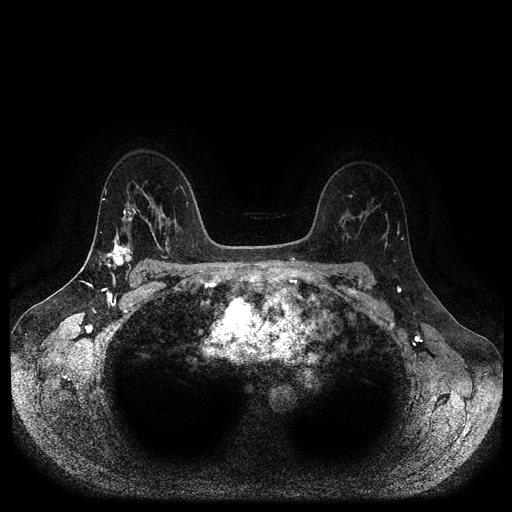
Breast MRI (dynamic contrast-enhanced, multi-phase), one axial slice; position 70 of 116 along the scan axis; dynamic contrast-enhanced series, time point 2 of 5 at this slice position (early post-contrast); 1.5 T; TE 2.6 ms, TR 5.3 ms; 2 mm slice thickness; 512 × 512 image matrix, field of view 360 × 360 mm. Patient: female, 45 years.
Outlined on this slice (semi-automatic segmentation, software-assisted and operator-edited):
- breast lesion (labelled 'tumour' in the annotation; benign lesions carry a separate 'benign' label): bounding box (x1, y1, x2, y2) in pixels: (104, 241, 134, 268)